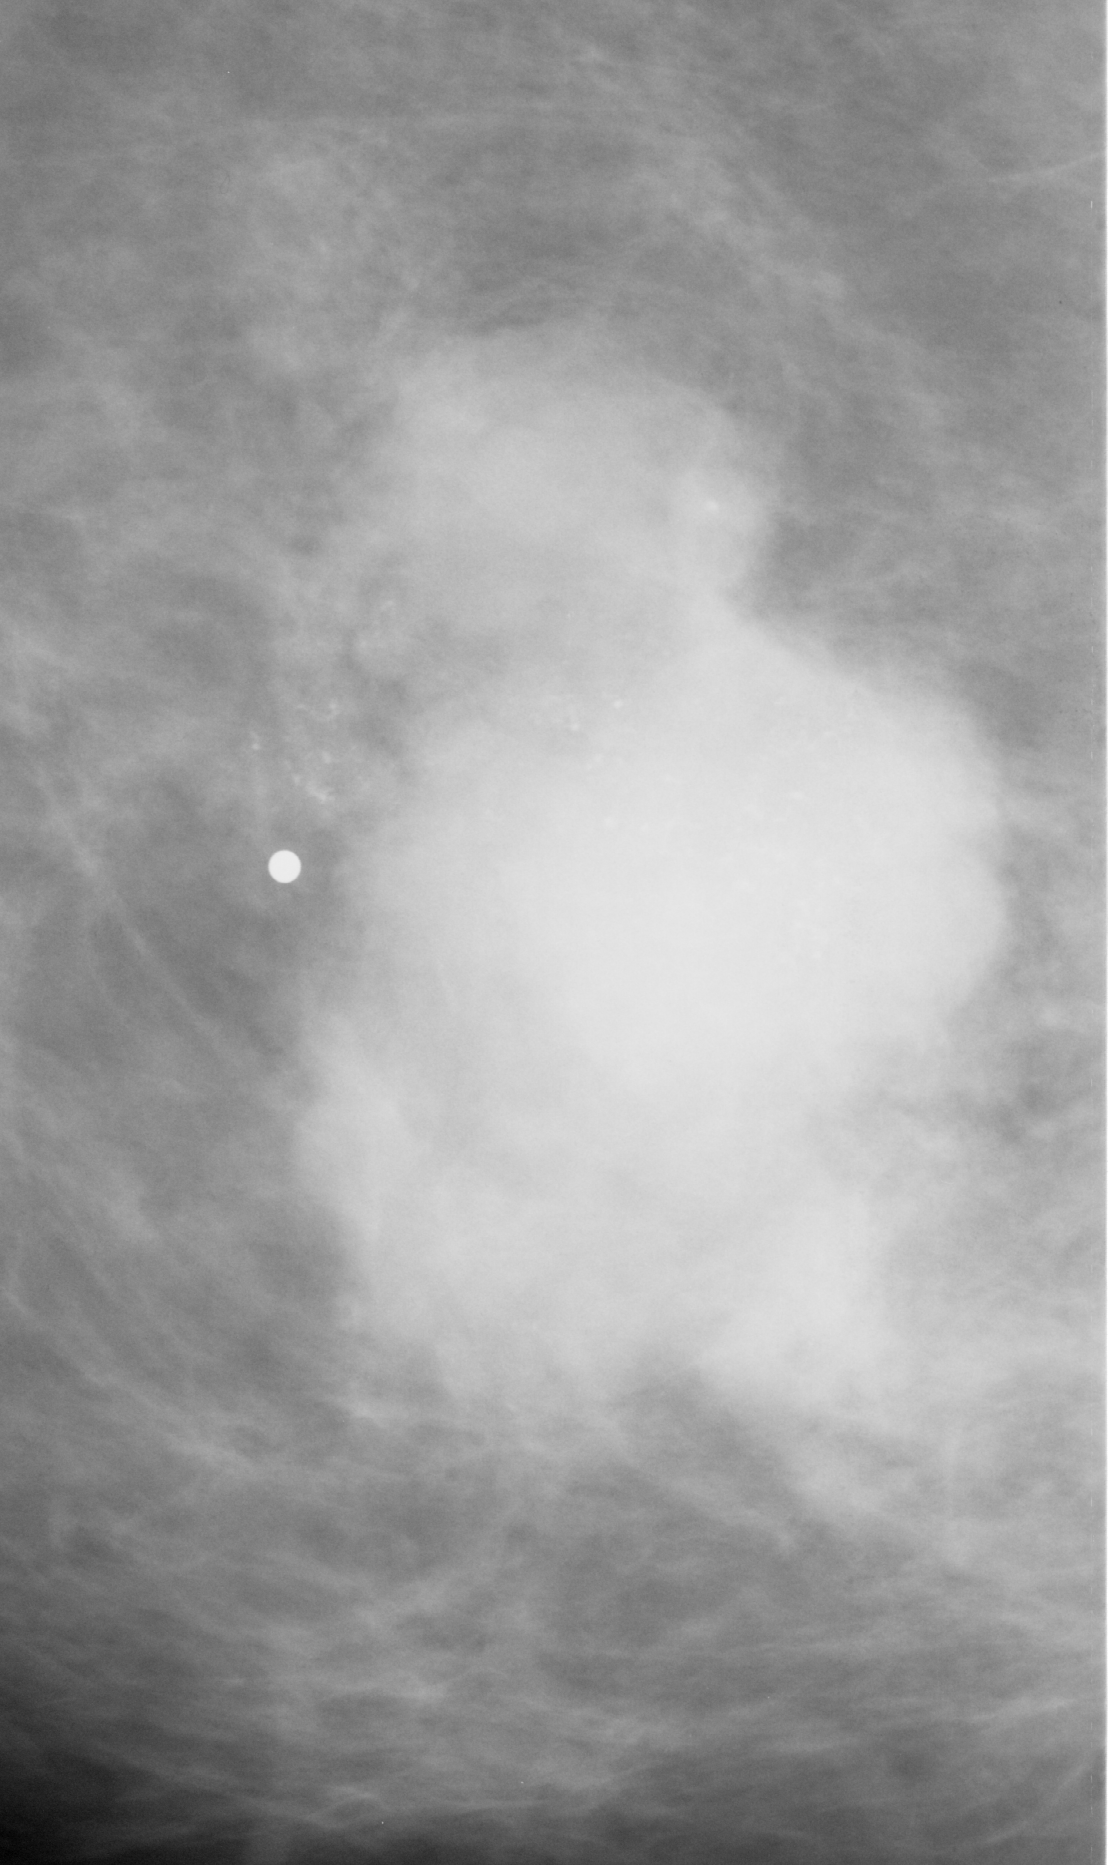
Crop from a digitized film mammogram around one marked abnormality, right breast, CC view, BI-RADS breast density category 1 (scale 1–4).
- Marked abnormality: calcifications, morphology pleomorphic, distribution clustered; BI-RADS assessment category 5; pathology (as recorded): malignant.